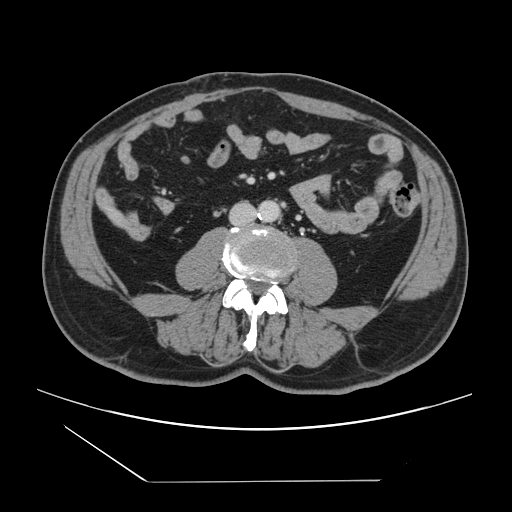
Contrast-enhanced abdominal CT, one axial slice; slice 10 of 157 in the series (ordered by position); 120 kVp; intravenous contrast given; soft-tissue window (W 400 / L 40 HU); 2.5 mm slice thickness; 512 × 512 image matrix, field of view 407 × 407 mm. Male patient, age 61 years. Case-level facts recorded for this patient, not image findings: diagnosis: colorectal cancer liver metastases, imaged before liver resection; multiple liver metastases: yes; largest metastasis: 5.5 cm; chemotherapy before resection: no.
Annotated regions visible in this slice (expert manual segmentation):
- liver: bounding box <109,209,121,223> (left, top, right, bottom; pixels)
- planned liver remnant (the part of the liver to remain after resection): <110,210,114,213>